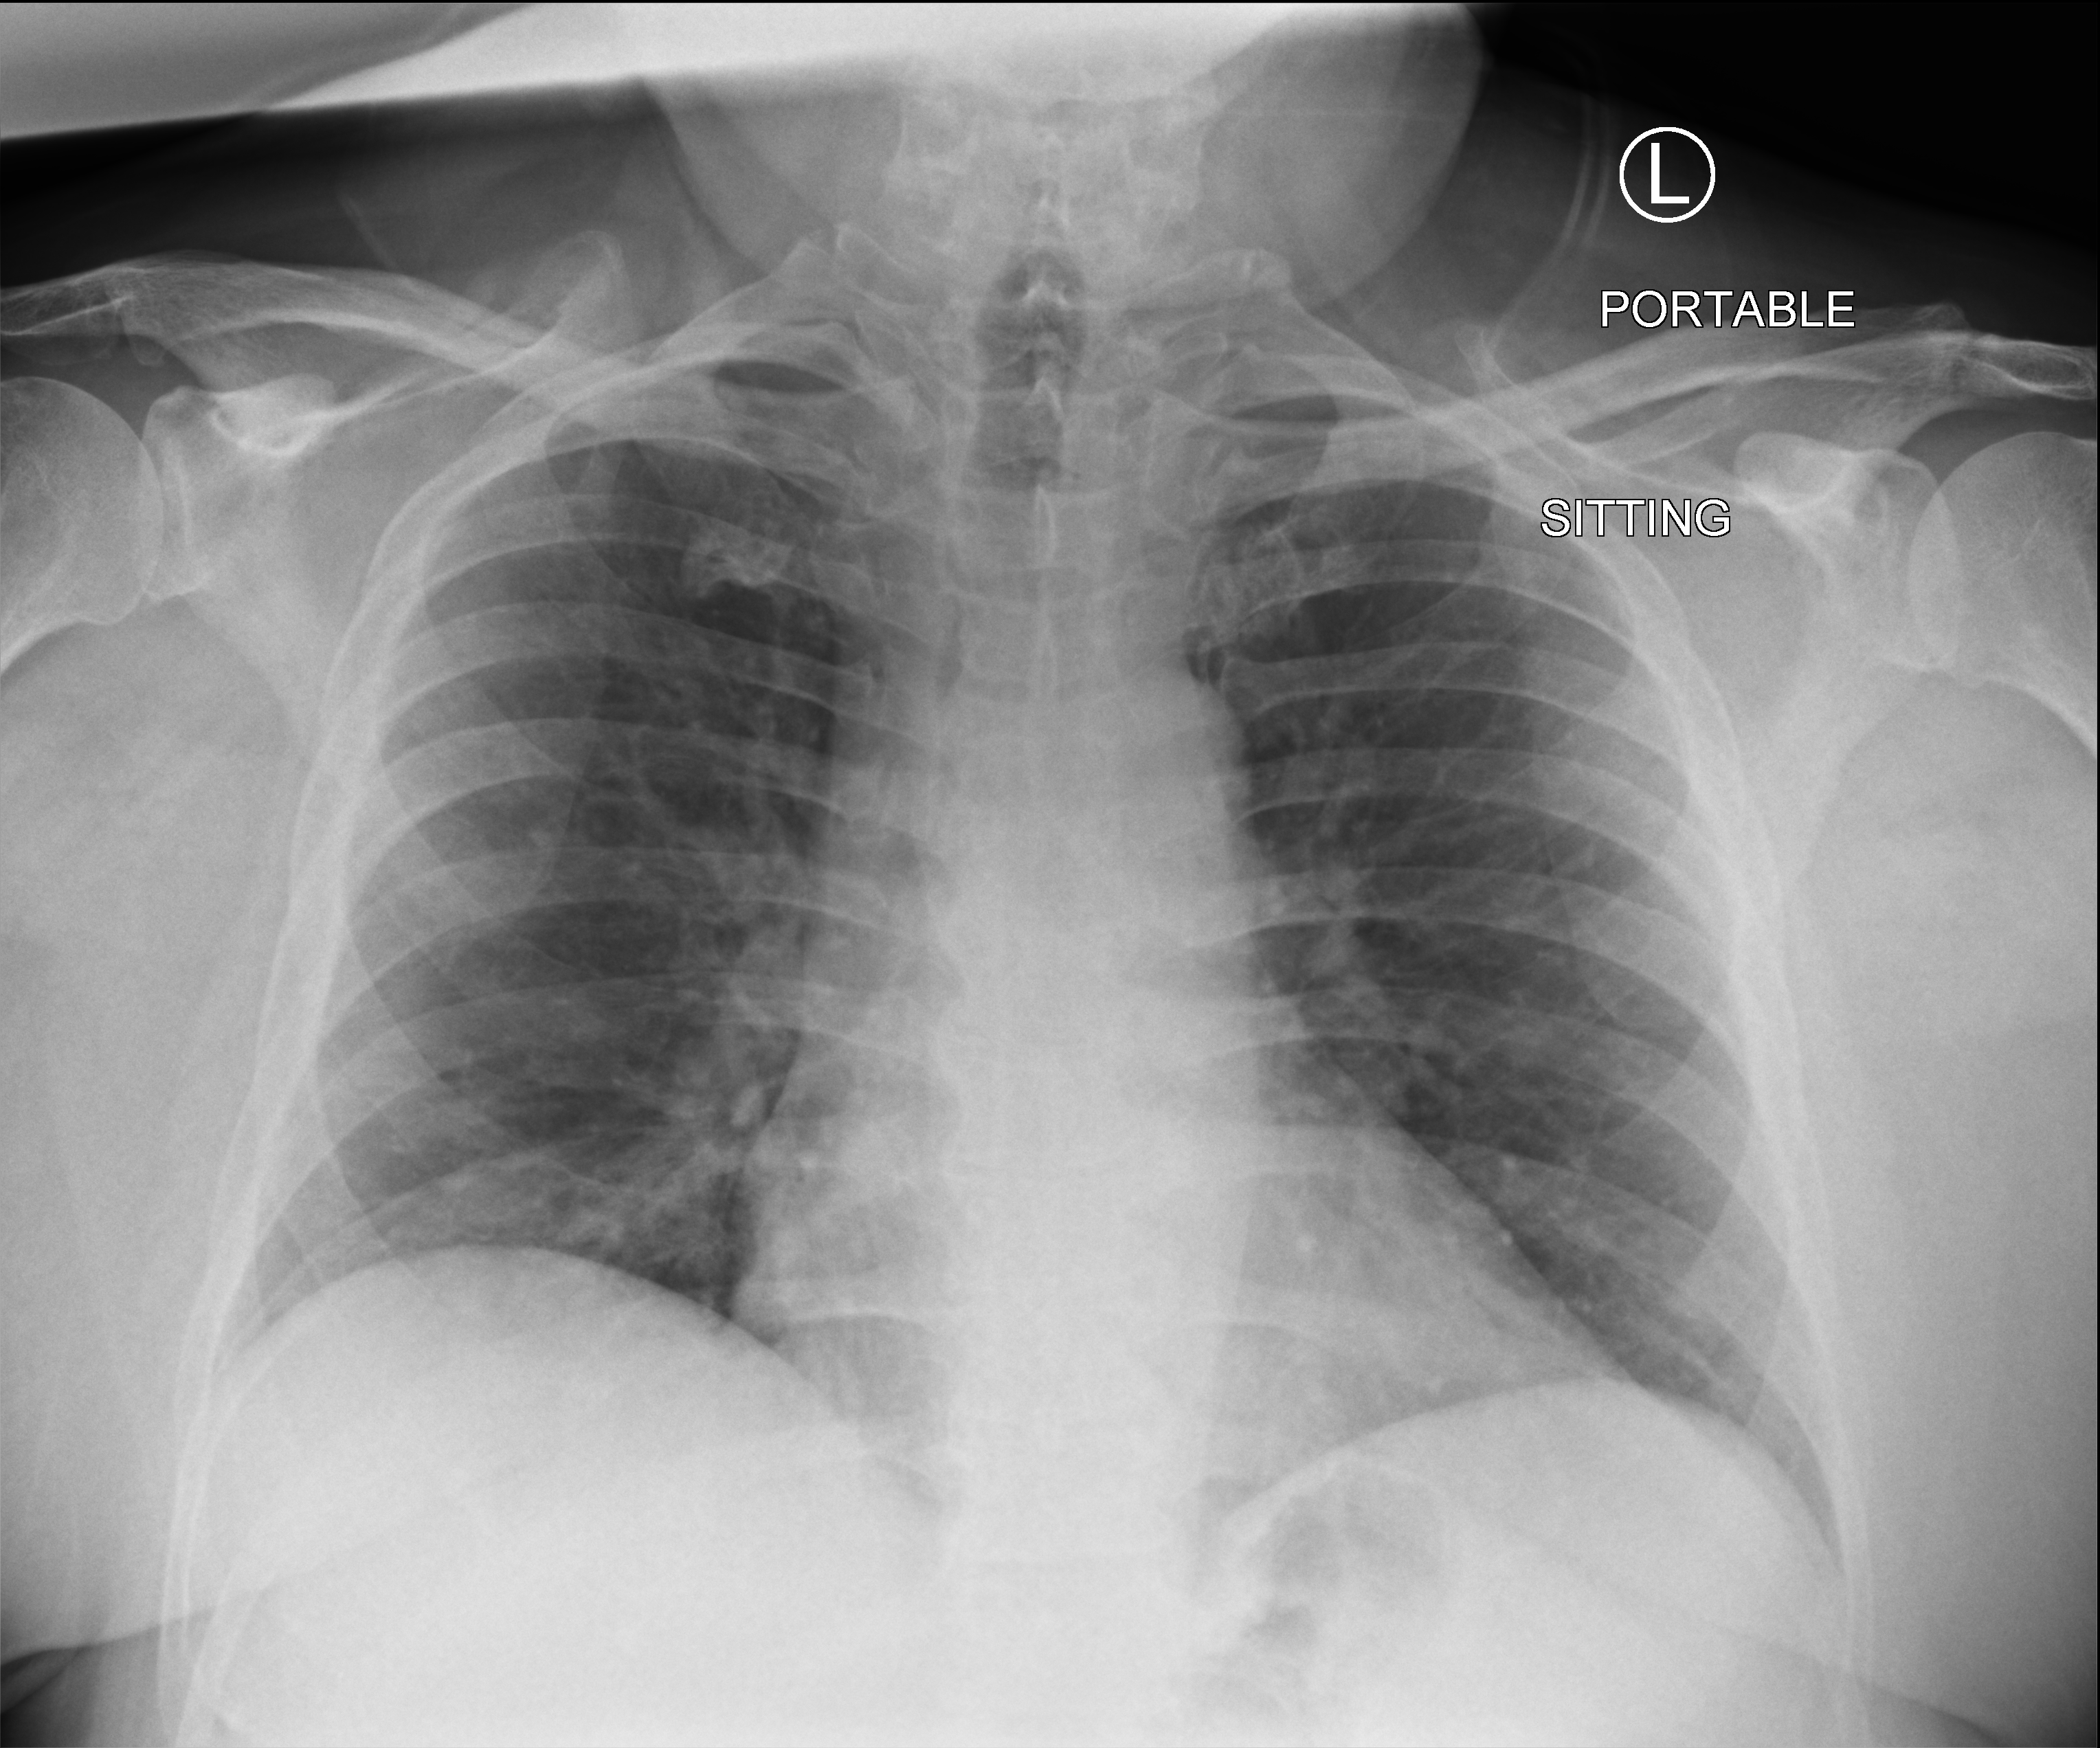
Portable chest radiograph; anteroposterior (AP) projection. Patient hospitalised with COVID-19; male, aged 60–74 years.
Admission-level facts for this patient (not findings on this image; timing relative to this image not recorded):
- COPD (admission record): no
- admitted to intensive care during this hospital stay: no